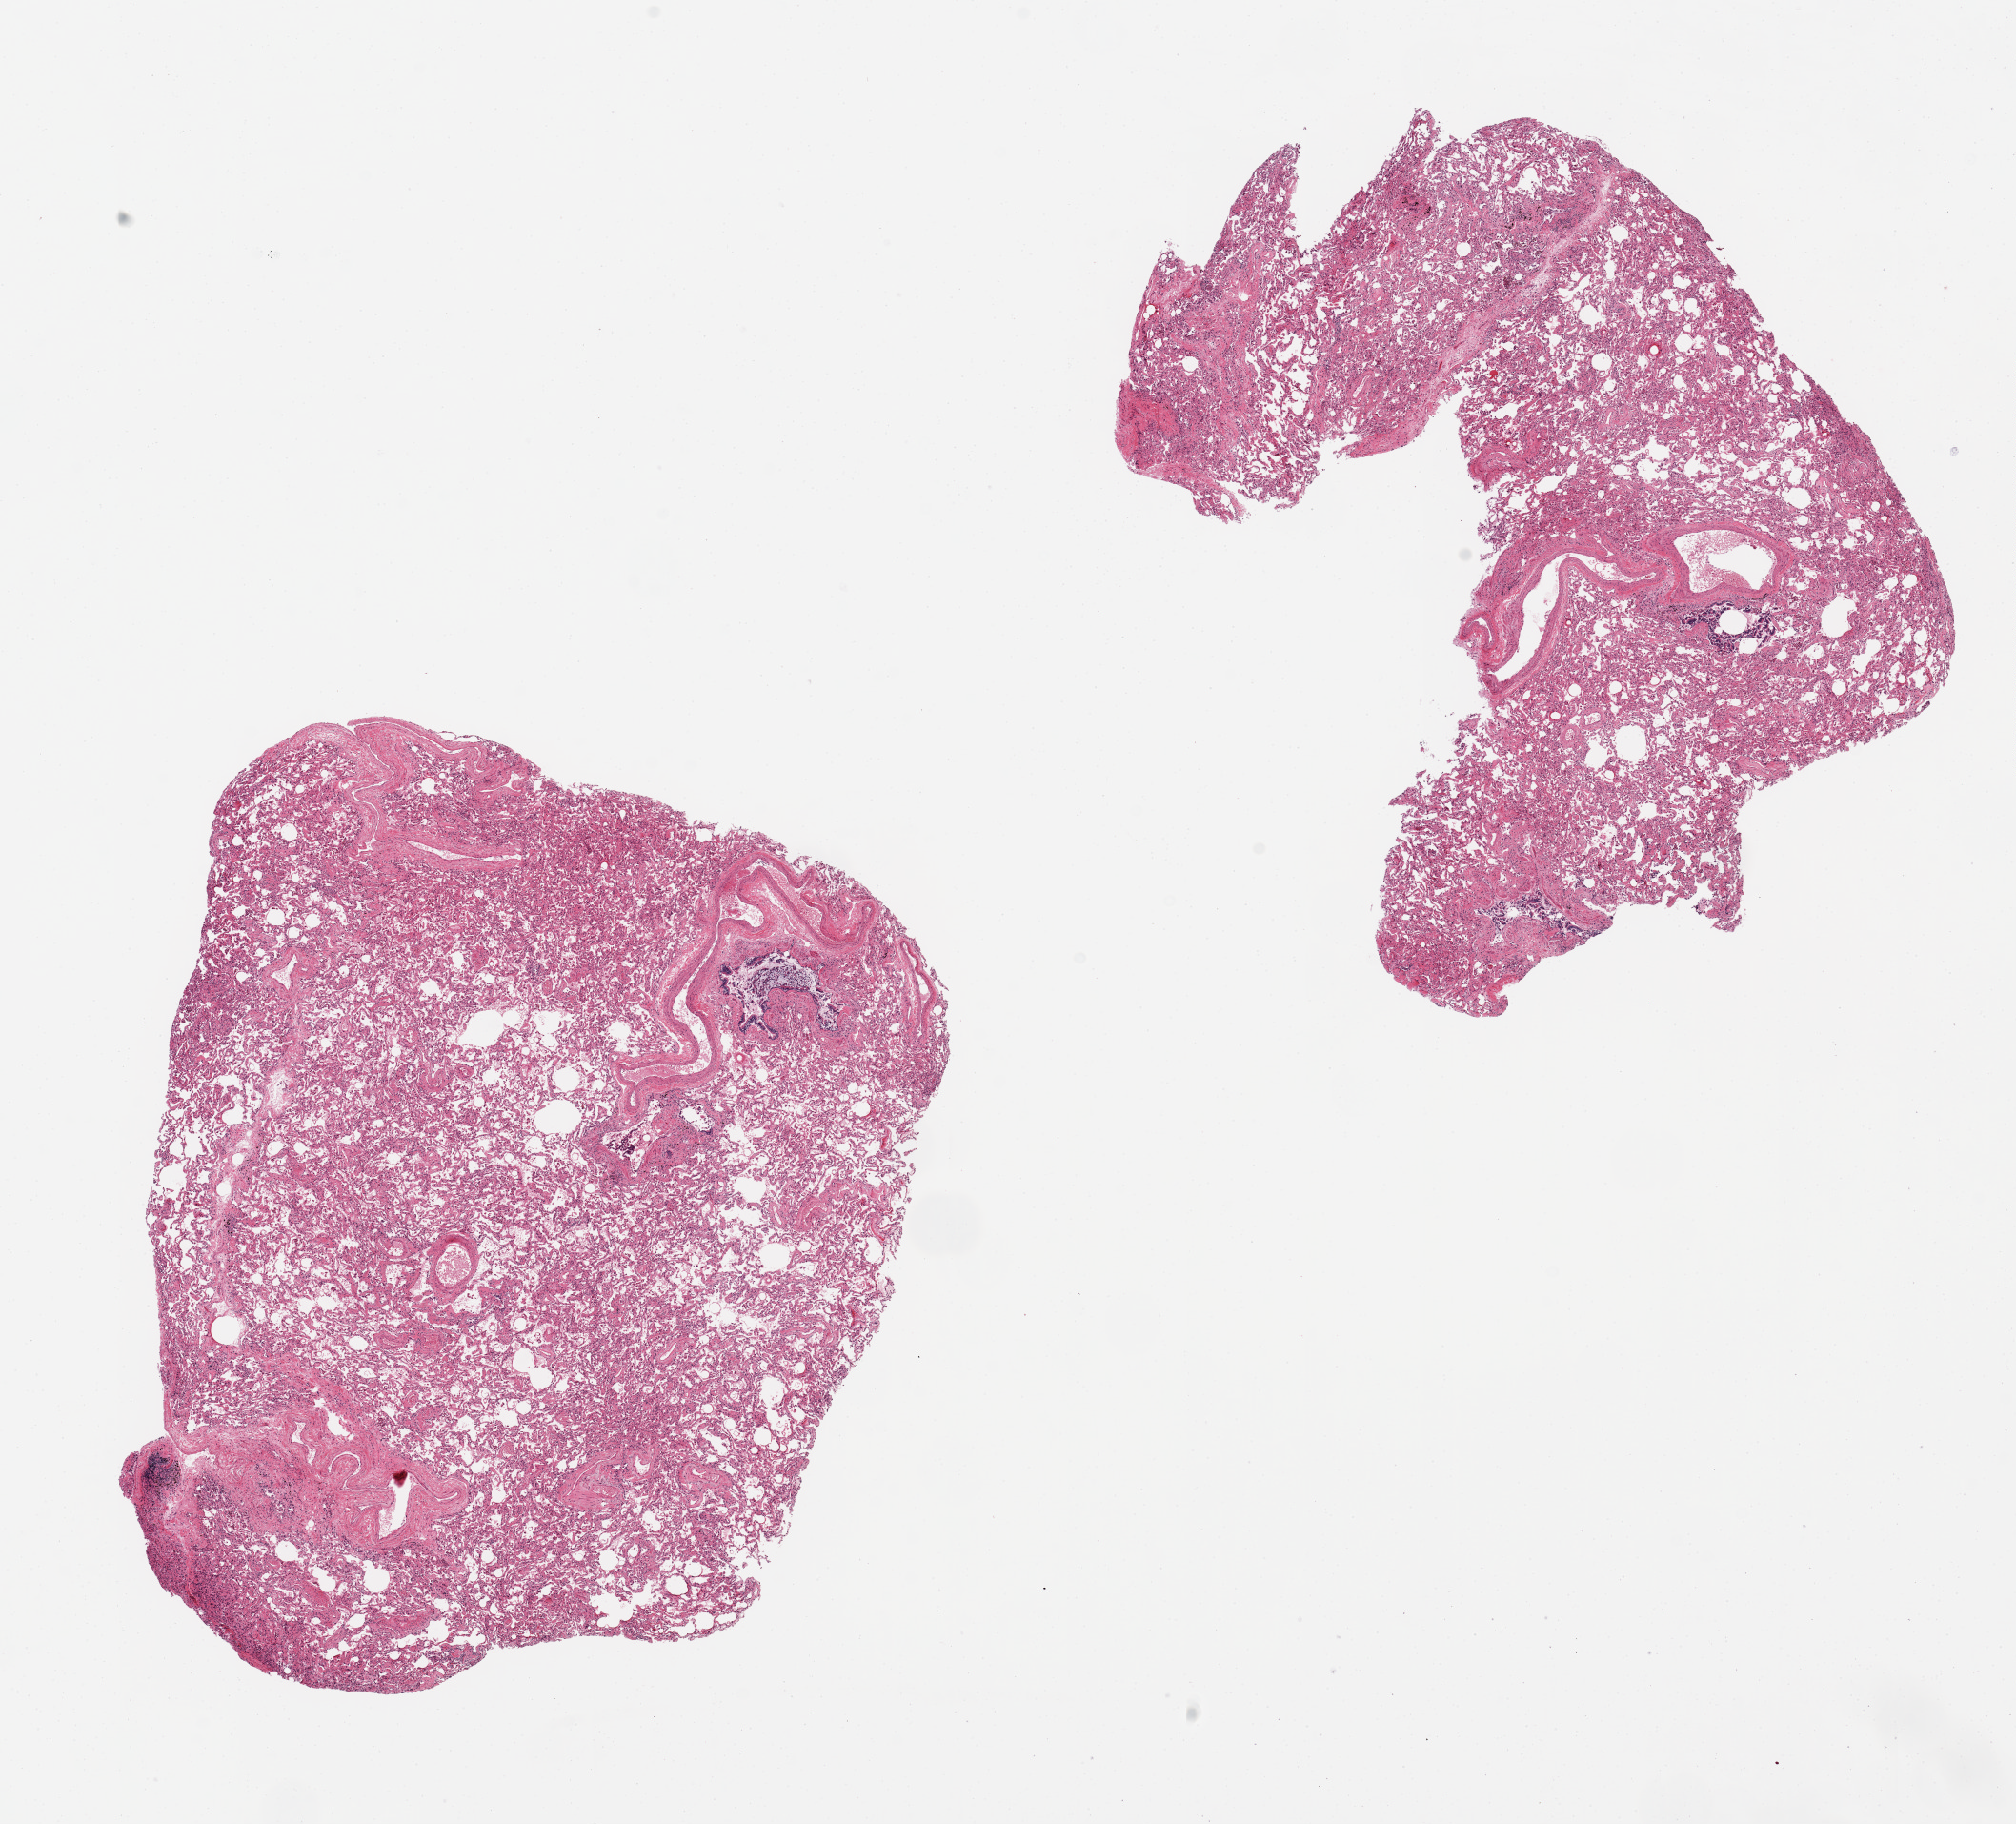
H&E whole-slide image, low-resolution overview of the scanned area, about 16.7 x 15.1 mm (acquisition: 20x scan). PAXgene-fixed paraffin-embedded (PFPE) section. Section of lung (target tissue). Tissue donor sample. Female donor.
Pathologist's review note for this sample: 2 pieces. 8x6.5 & 7x6mm; heart failure cells.